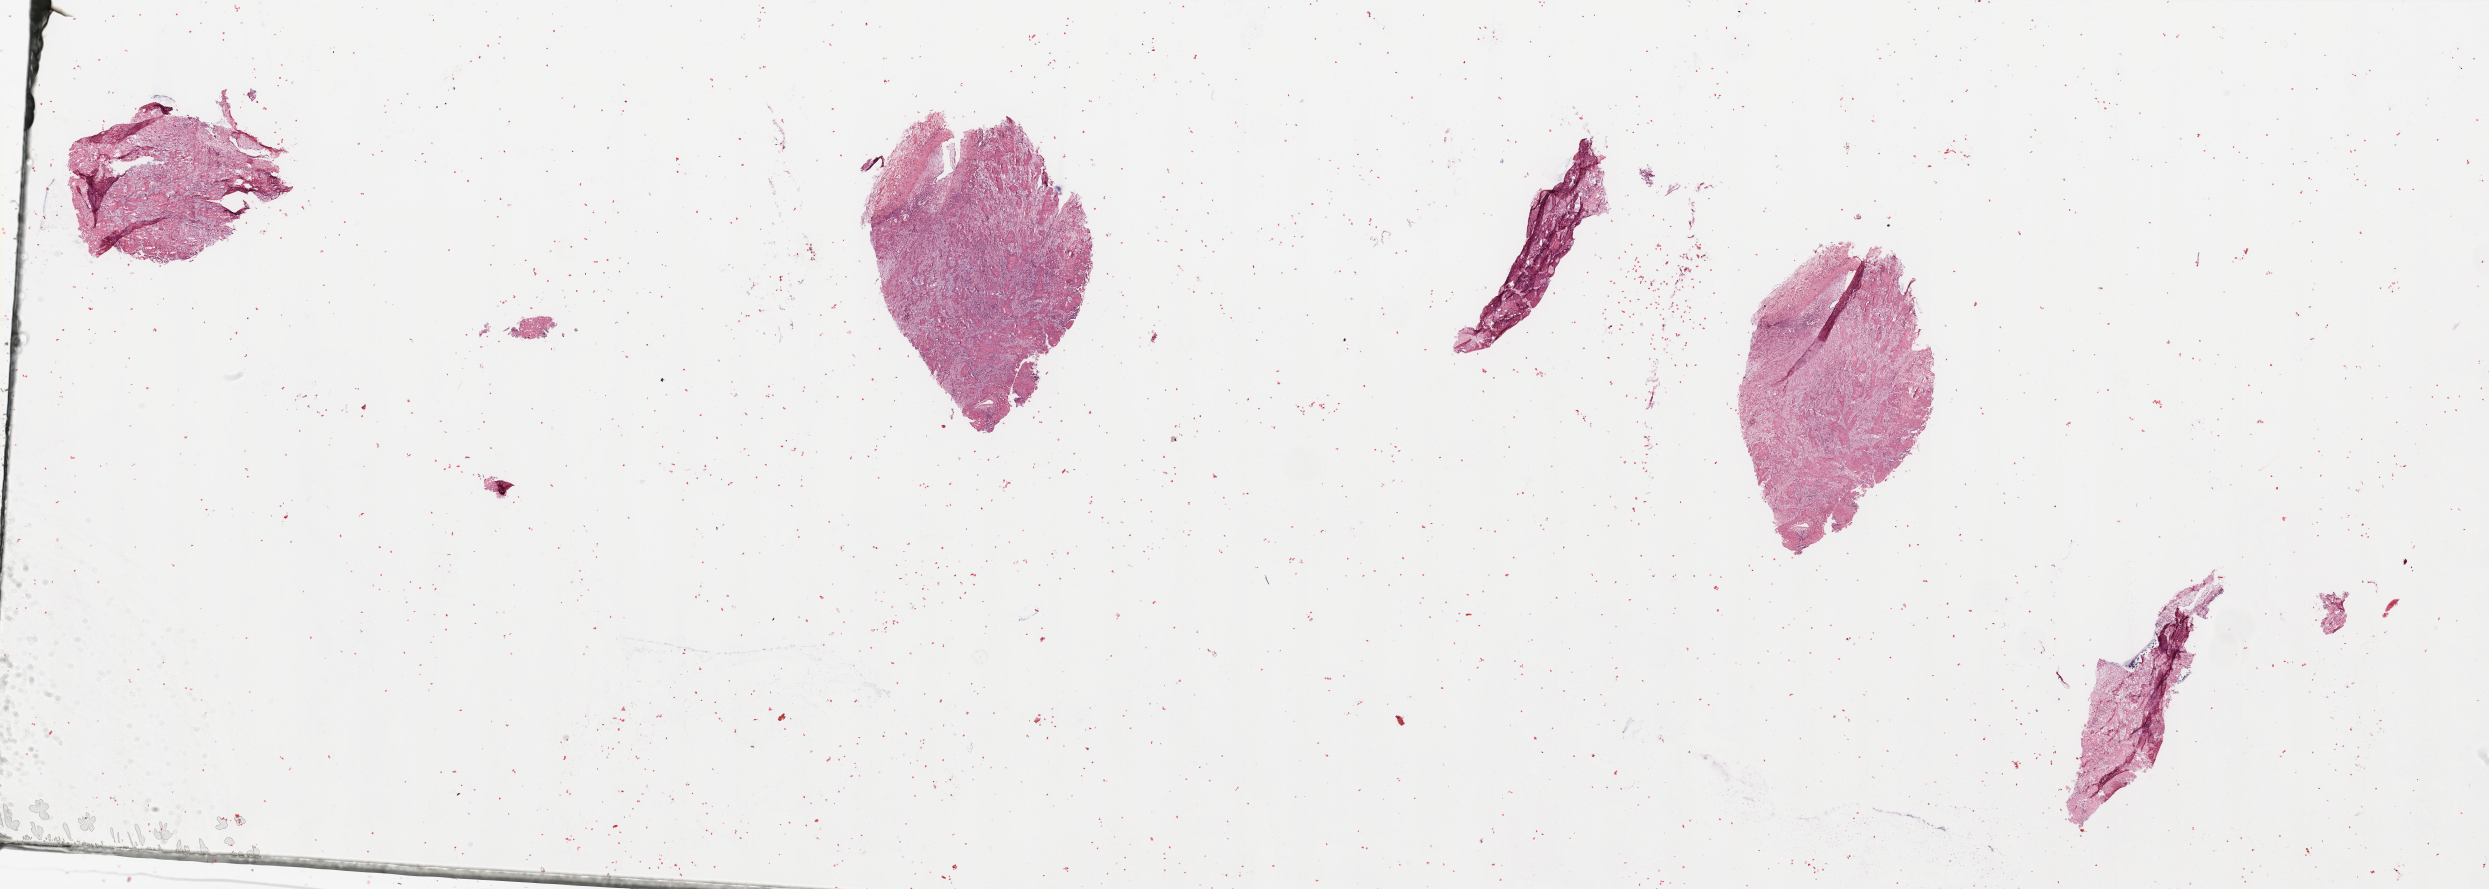
Whole-slide histology image, H&E, a low-resolution overview of the entire scanned area, about 39.4 x 14.1 mm (slide scanned at 20x). Lung, tumour tissue. Patient: male, age 70 years. Histologic grade: G2 (moderately differentiated).
• AJCC pathologic stage: IIIA
• histologic diagnosis: Squamous cell carcinoma, NOS
• primary tumour site (as recorded): left upper lobe